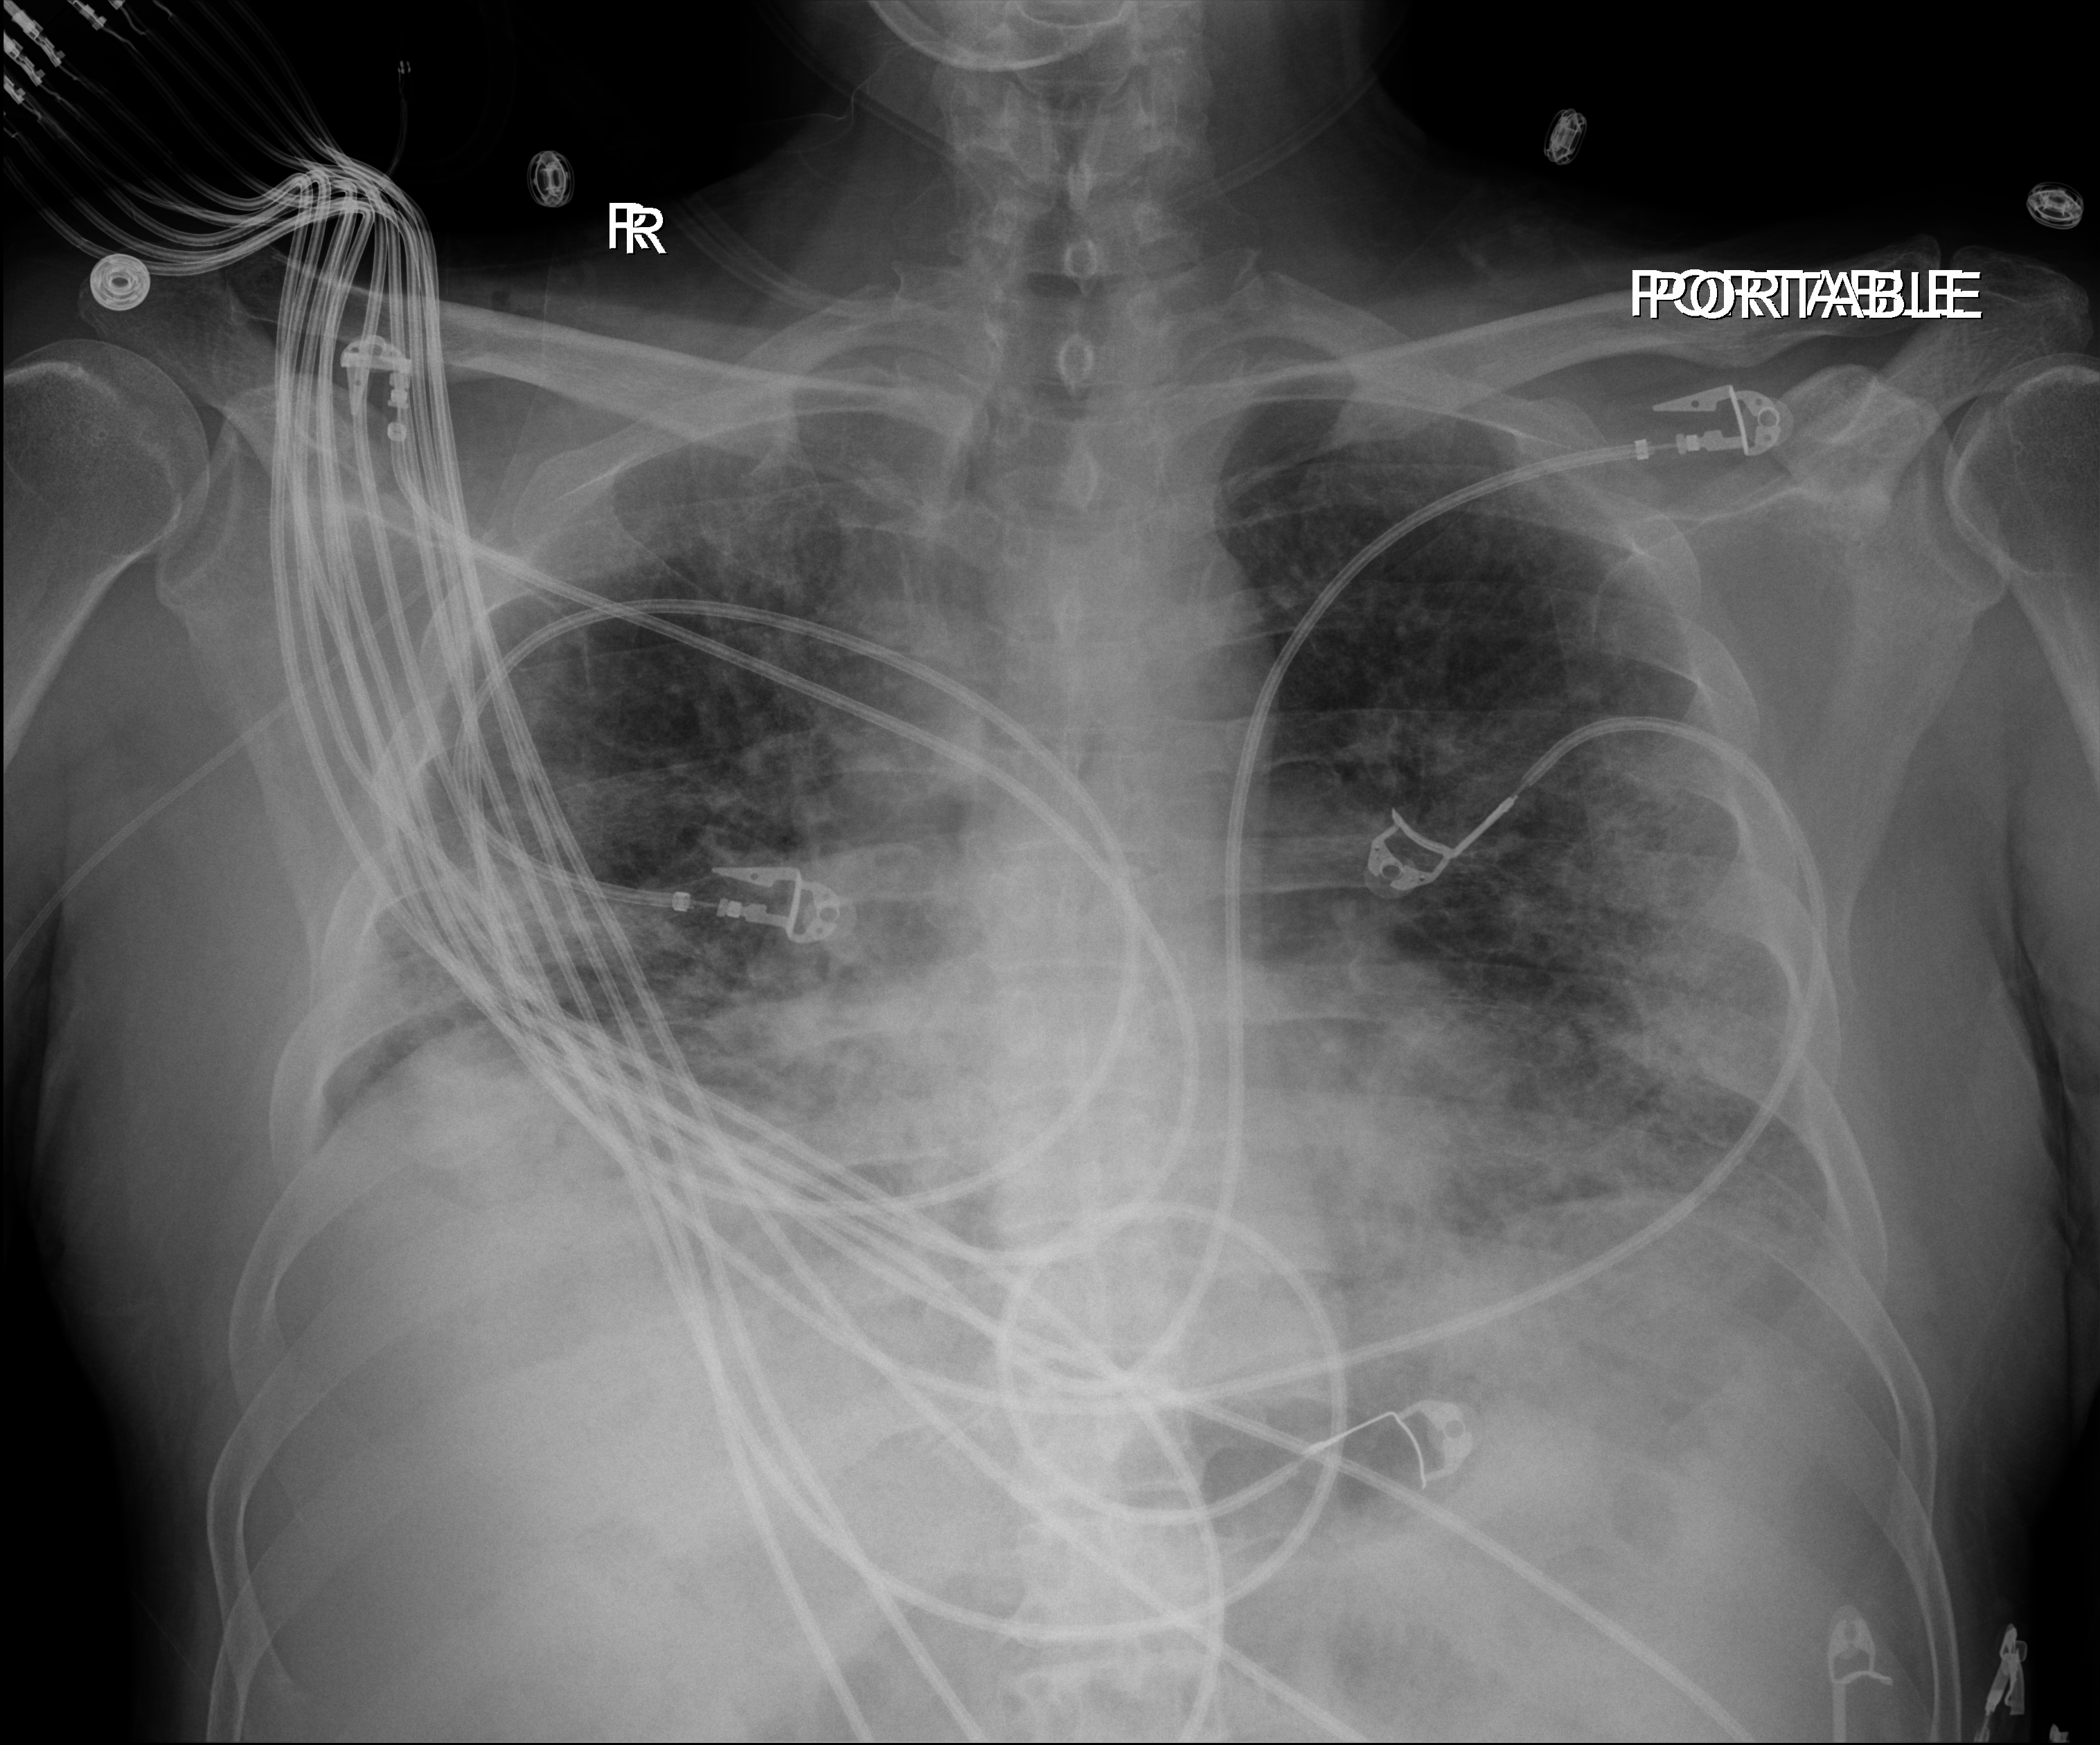
Chest X-ray (portable), anteroposterior (AP) projection. Male patient hospitalised with COVID-19, age 18–59 years.
Hospital-stay facts (about this admission, not read from this image; timing relative to this image not recorded):
- admitted to intensive care during this hospital stay: yes
- mechanically ventilated during this hospital stay: yes